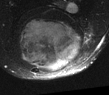
MRI of an extremity soft-tissue mass, one axial slice; slice 31 of 52 in the series (ordered by position); T2-weighted fat-saturated; MR volume resampled by the dataset authors to the PET/CT grid (not the native acquisition matrix); 109 × 95 image matrix, field of view 106 × 93 mm. Male patient. From the clinical record (not read from this slice): histological type: synovial sarcoma; site of the primary tumour: left poplietal fossa.
Structures marked on this image (expert contour drawn on MRI and transferred to this co-registered scan by the dataset authors):
- gross tumour volume (mass): bounding box [x1, y1, x2, y2] px = [19, 19, 82, 71]